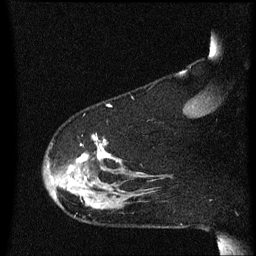
Breast MRI (dynamic contrast-enhanced), one sagittal slice; position 49 of 60 along the scan axis; dynamic contrast-enhanced series, image 2 of 3 at this slice position (ordered by acquisition); 1.5 T; TE 4.2 ms, TR 8.4 ms; 2 mm slice thickness; 256 × 256 image matrix, field of view 200 × 200 mm. Patient: female, 48 years.
Annotated regions visible in this slice (semi-automatic segmentation, software-assisted and operator-edited):
- analysis volume of interest (the breast-tissue region the enhancement analysis was run in; not a lesion): bounding box (x1, y1, x2, y2) in pixels: (44, 138, 134, 209)
- tumour enhancement mask (voxels above the 70 % enhancement threshold inside the analysis volume of interest): (68, 138, 110, 207)